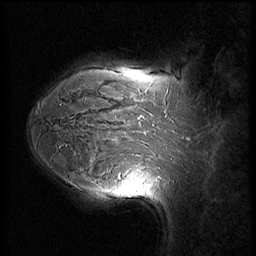
Breast MRI (dynamic contrast-enhanced), one sagittal slice; slice 46 of 60 in the series (ordered by position); dynamic contrast-enhanced series, image 2 of 3 at this slice position (ordered by acquisition); 1.5 T; TE 4.2 ms, TR 8.9 ms; 256 × 256 image matrix, field of view 220 × 220 mm. Female patient, age 37 years. Case-level facts recorded for this patient, not image findings: setting: breast cancer imaged before/during neoadjuvant chemotherapy; receptor status: triple-negative.
Structures marked on this image (semi-automatically segmented with operator editing):
- analysis volume of interest (the breast-tissue region the enhancement analysis was run in; not a lesion): bounding box <114,153,159,206> (left, top, right, bottom; pixels)
- tumour enhancement mask (voxels above the 140 % enhancement threshold inside the analysis volume of interest): <136,177,143,184>